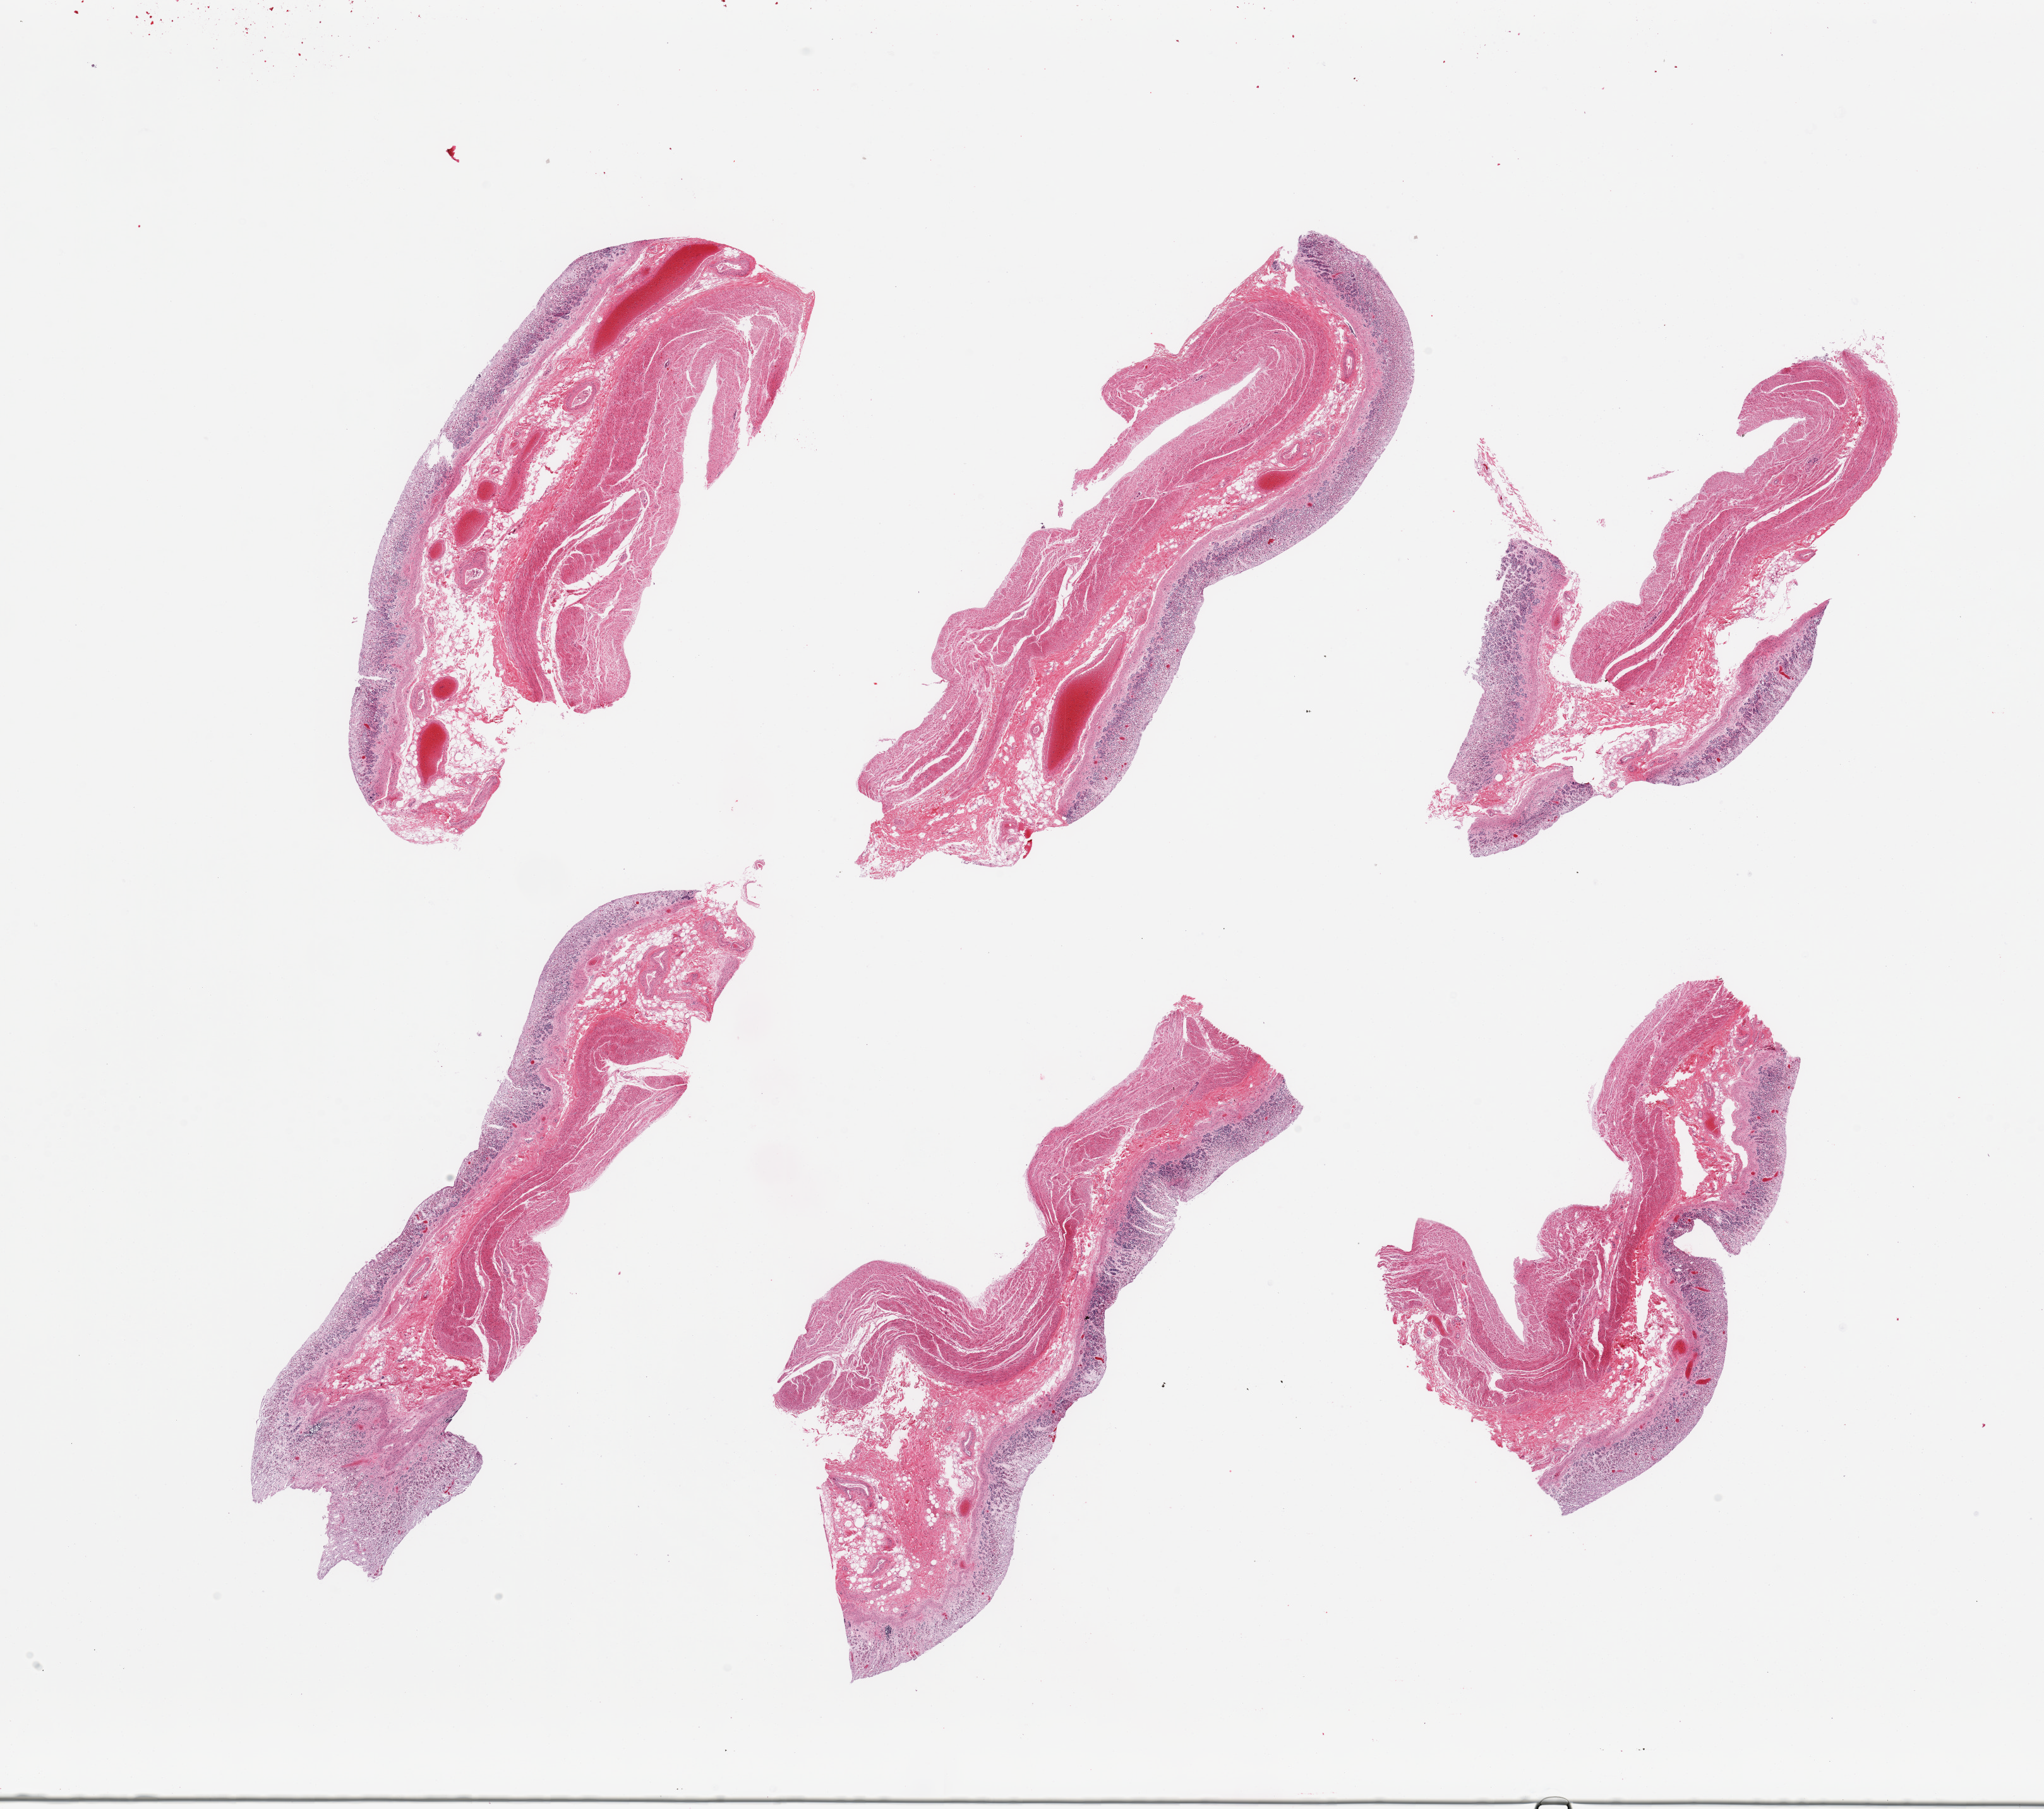
H&E whole-slide image — low-resolution overview of the scanned area, about 25.6 x 22.7 mm (slide scanned at 20x). PAXgene-fixed paraffin-embedded (PFPE) section. Sampled site (target tissue): stomach. Tissue donor sample. Donor: male.
* pathologist's review note for this sample: 6 pieces; mucosa severely autolyzed, muscle intact